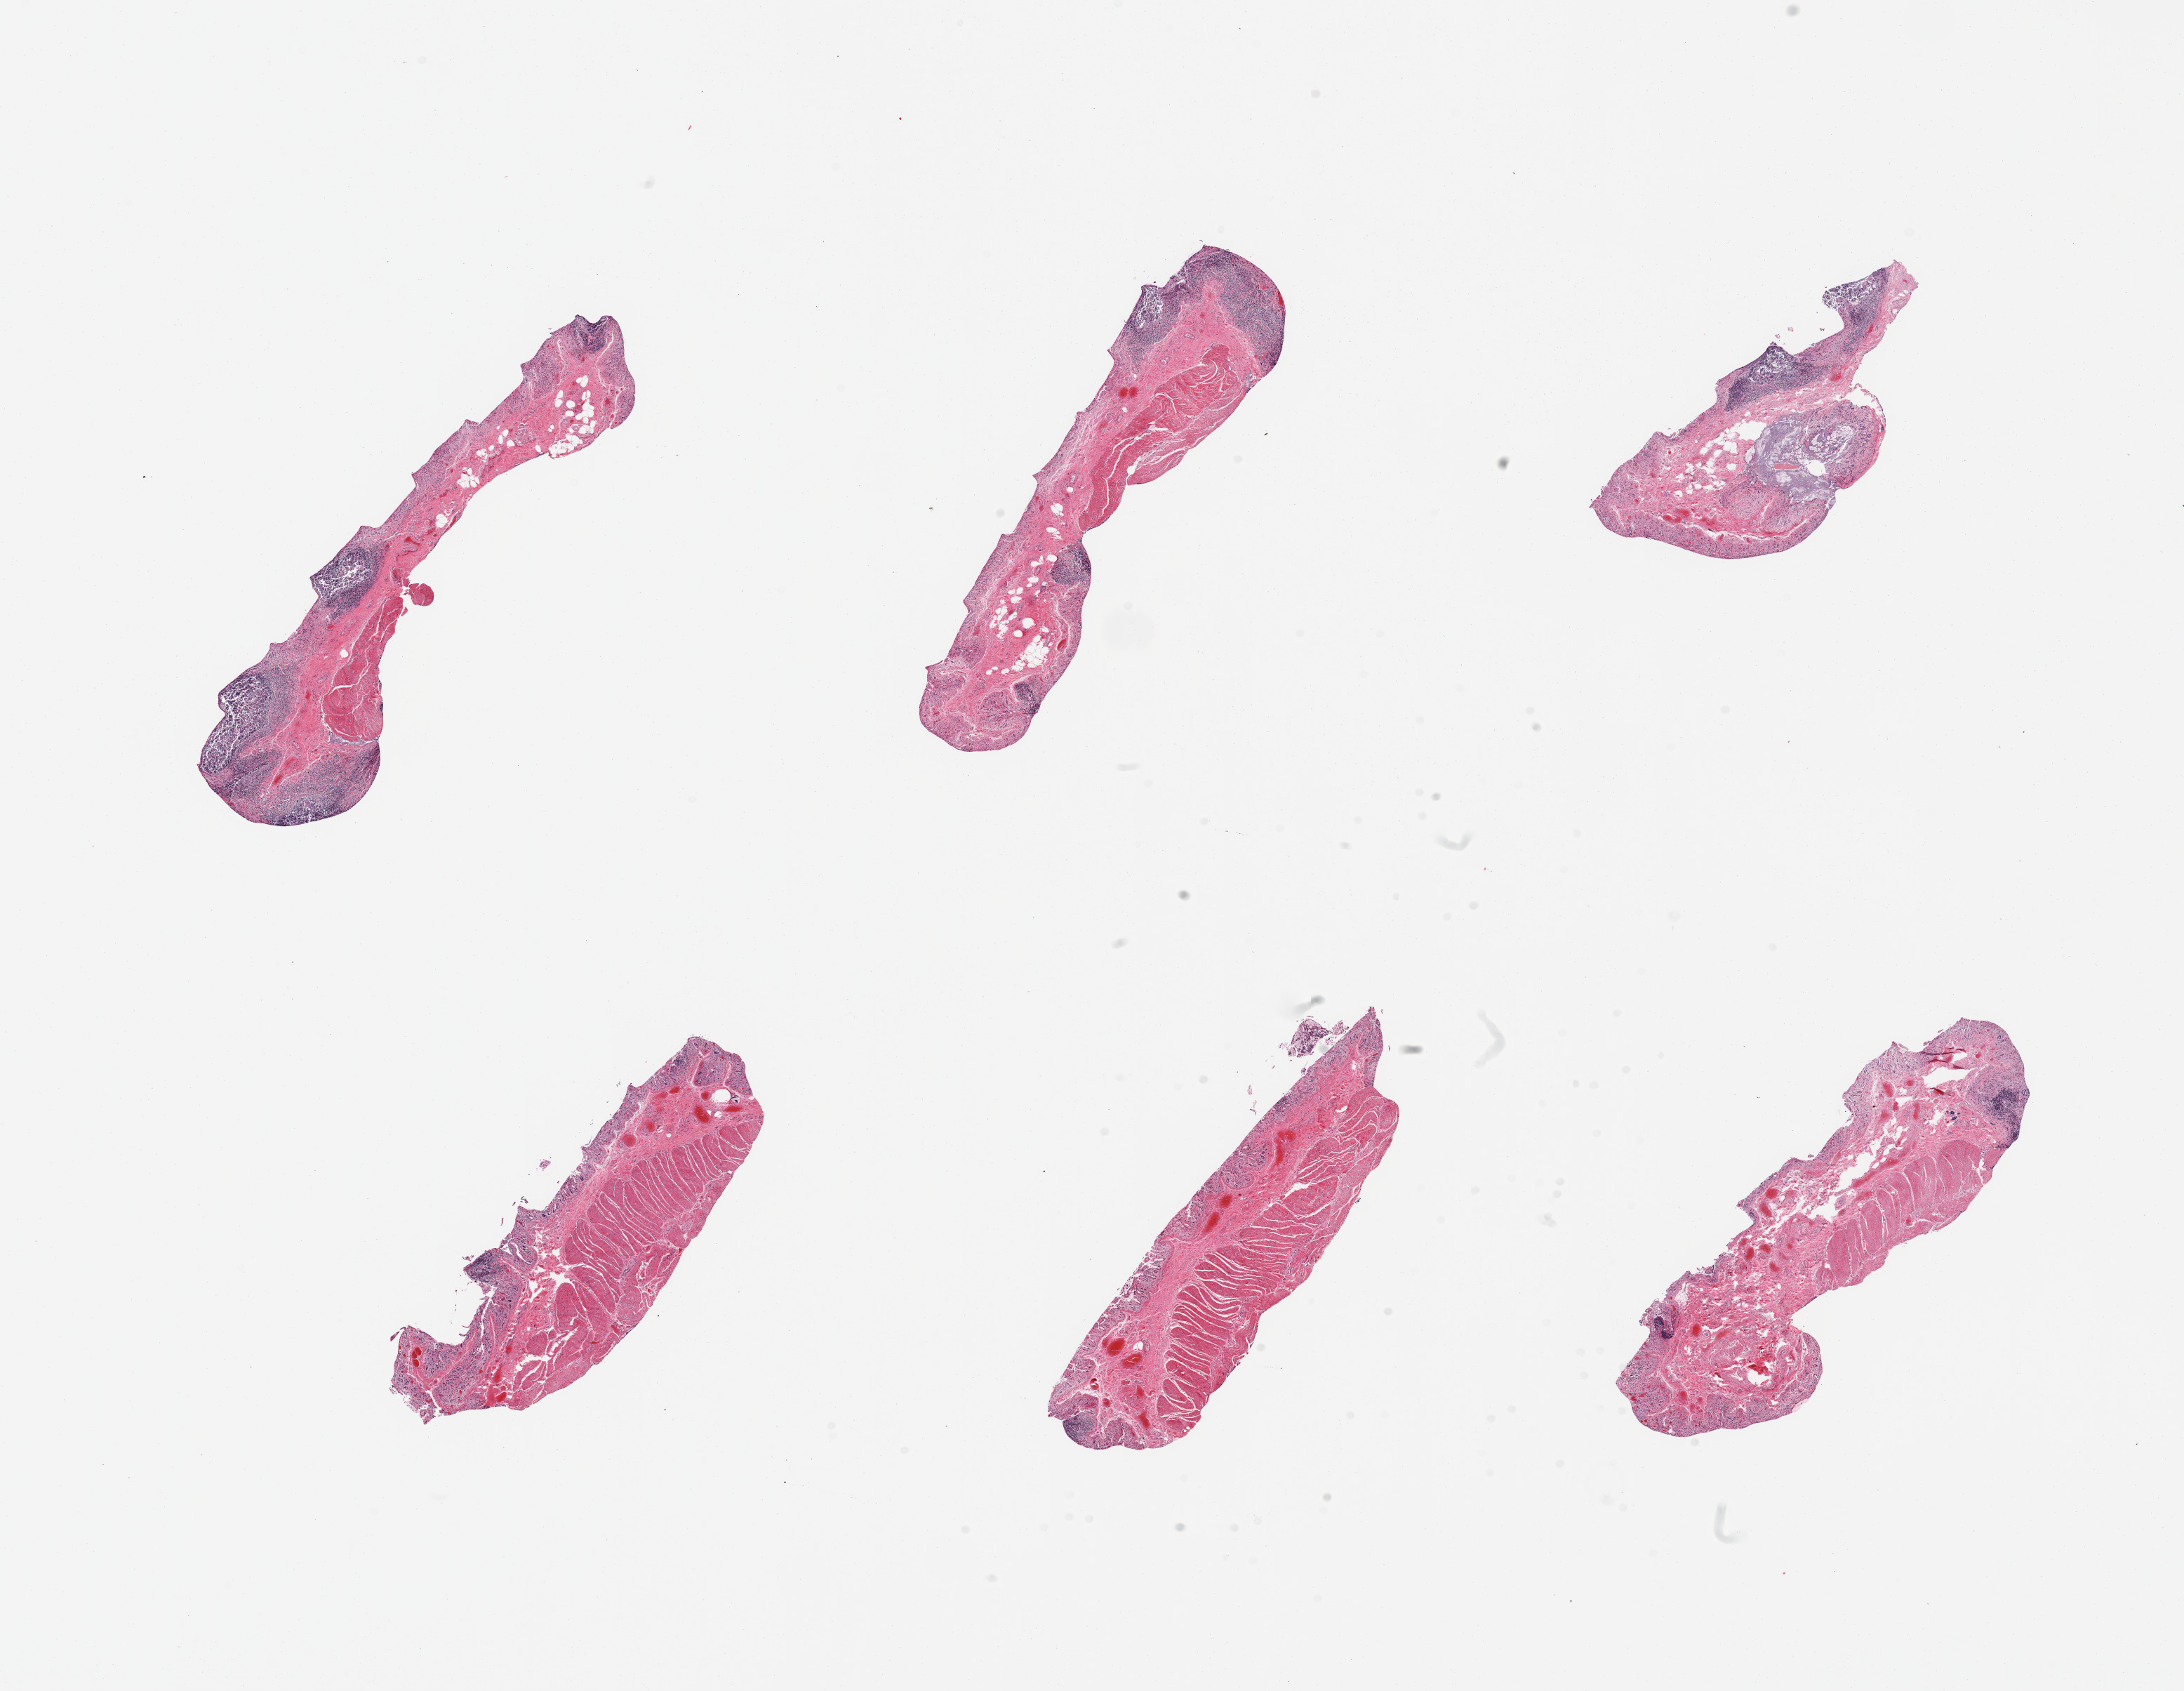
Haematoxylin and eosin whole-slide image, brightfield — a low-resolution overview of the entire scanned area, about 24.6 x 19.1 mm. PAXgene-fixed paraffin-embedded (PFPE) section. Section of ileum (target tissue). Tissue donor sample.
* review note (as recorded): 6 piecesm glandular mucosa sloughed/autolyzed; ~20% residual target lymphoid aggregates